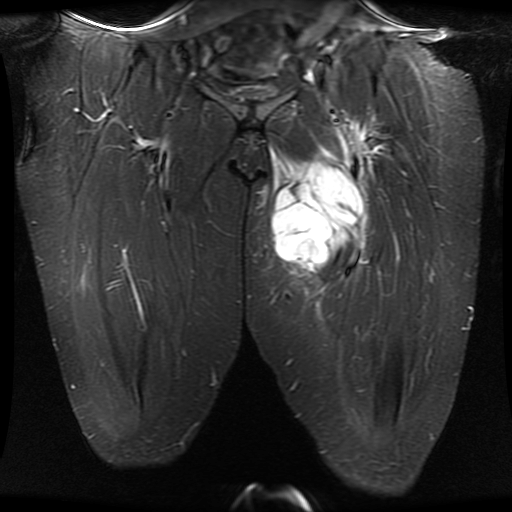
MRI of an extremity soft-tissue mass, one coronal slice; position 9 of 30 along the scan axis; STIR; 5 mm slice thickness; 512 × 512 image matrix, field of view 460 × 460 mm. Female patient. Case-level facts recorded for this patient, not image findings: histological type: myxofibrosarcoma; grade: intermediate; site of the primary tumour: left thigh.
Outlined on this slice (manually delineated by an expert):
- gross tumour volume including surrounding oedema: box from (x=269, y=113) to (x=371, y=279) px
- gross tumour volume (mass): (x=270, y=163)–(x=365, y=279)